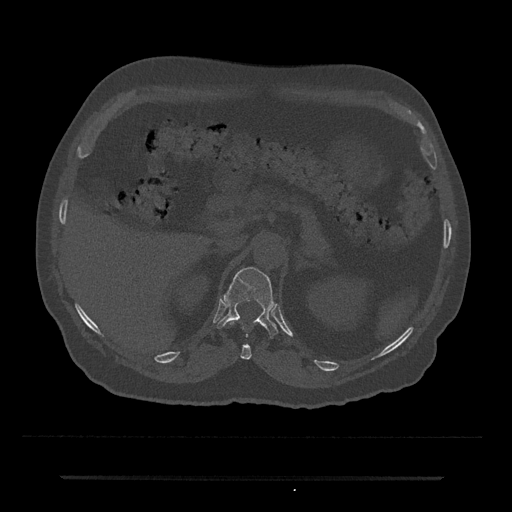
CT including the spine, one axial slice. Slice 142 of 797 in the series (ordered by position). Reconstruction kernel Br40s/3. Bone window (W 1800 / L 400 HU). 512 × 512 image matrix, field of view 437 × 437 mm. Male patient, age 69 years. Case-level facts recorded for this patient, not image findings: primary cancer: prostate.
Annotated regions visible in this slice (semi-automatic segmentation, software-assisted and operator-edited):
- T11 vertebra: bounding box (x1, y1, x2, y2) in pixels: (229, 321, 252, 360)
- T12 vertebra: (217, 267, 278, 338)